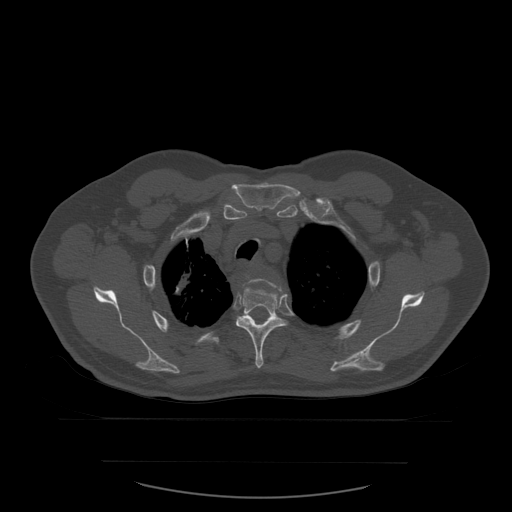
CT including the spine, one axial slice. Position 443 of 590 along the scan axis. Bone window (W 1800 / L 400 HU). 1.25 mm slice thickness. 512 × 512 image matrix, field of view 479 × 479 mm. Patient age 71 years. From the clinical record (not read from this slice): primary cancer: lung.
Annotated regions visible in this slice (semi-automatically segmented with operator editing):
- T3 vertebra: bounding box <247,276,282,293> (left, top, right, bottom; pixels)
- T4 vertebra: <236,279,287,369>